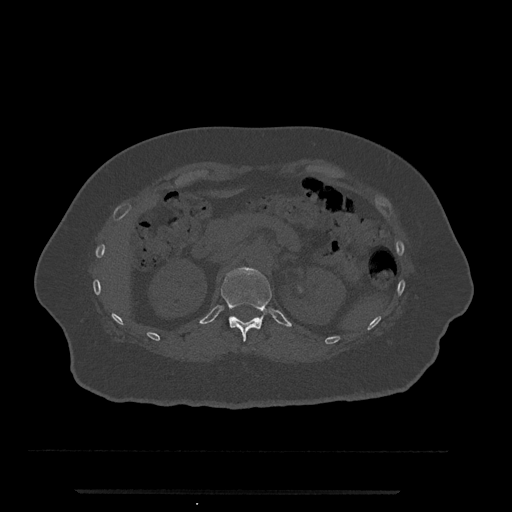
CT including the spine, one axial slice; slice 162 of 797 in the series (ordered by position); reconstruction kernel Br40s/3; 120 kVp; bone window (W 1800 / L 400 HU); 0.5 mm slice thickness; 512 × 512 image matrix, field of view 440 × 440 mm. Patient: female, 51 years. From the clinical record (not read from this slice): primary cancer: neuro.
Outlined on this slice (semi-automatically segmented with operator editing):
- T12 vertebra: bounding box <221,267,272,341> (left, top, right, bottom; pixels)